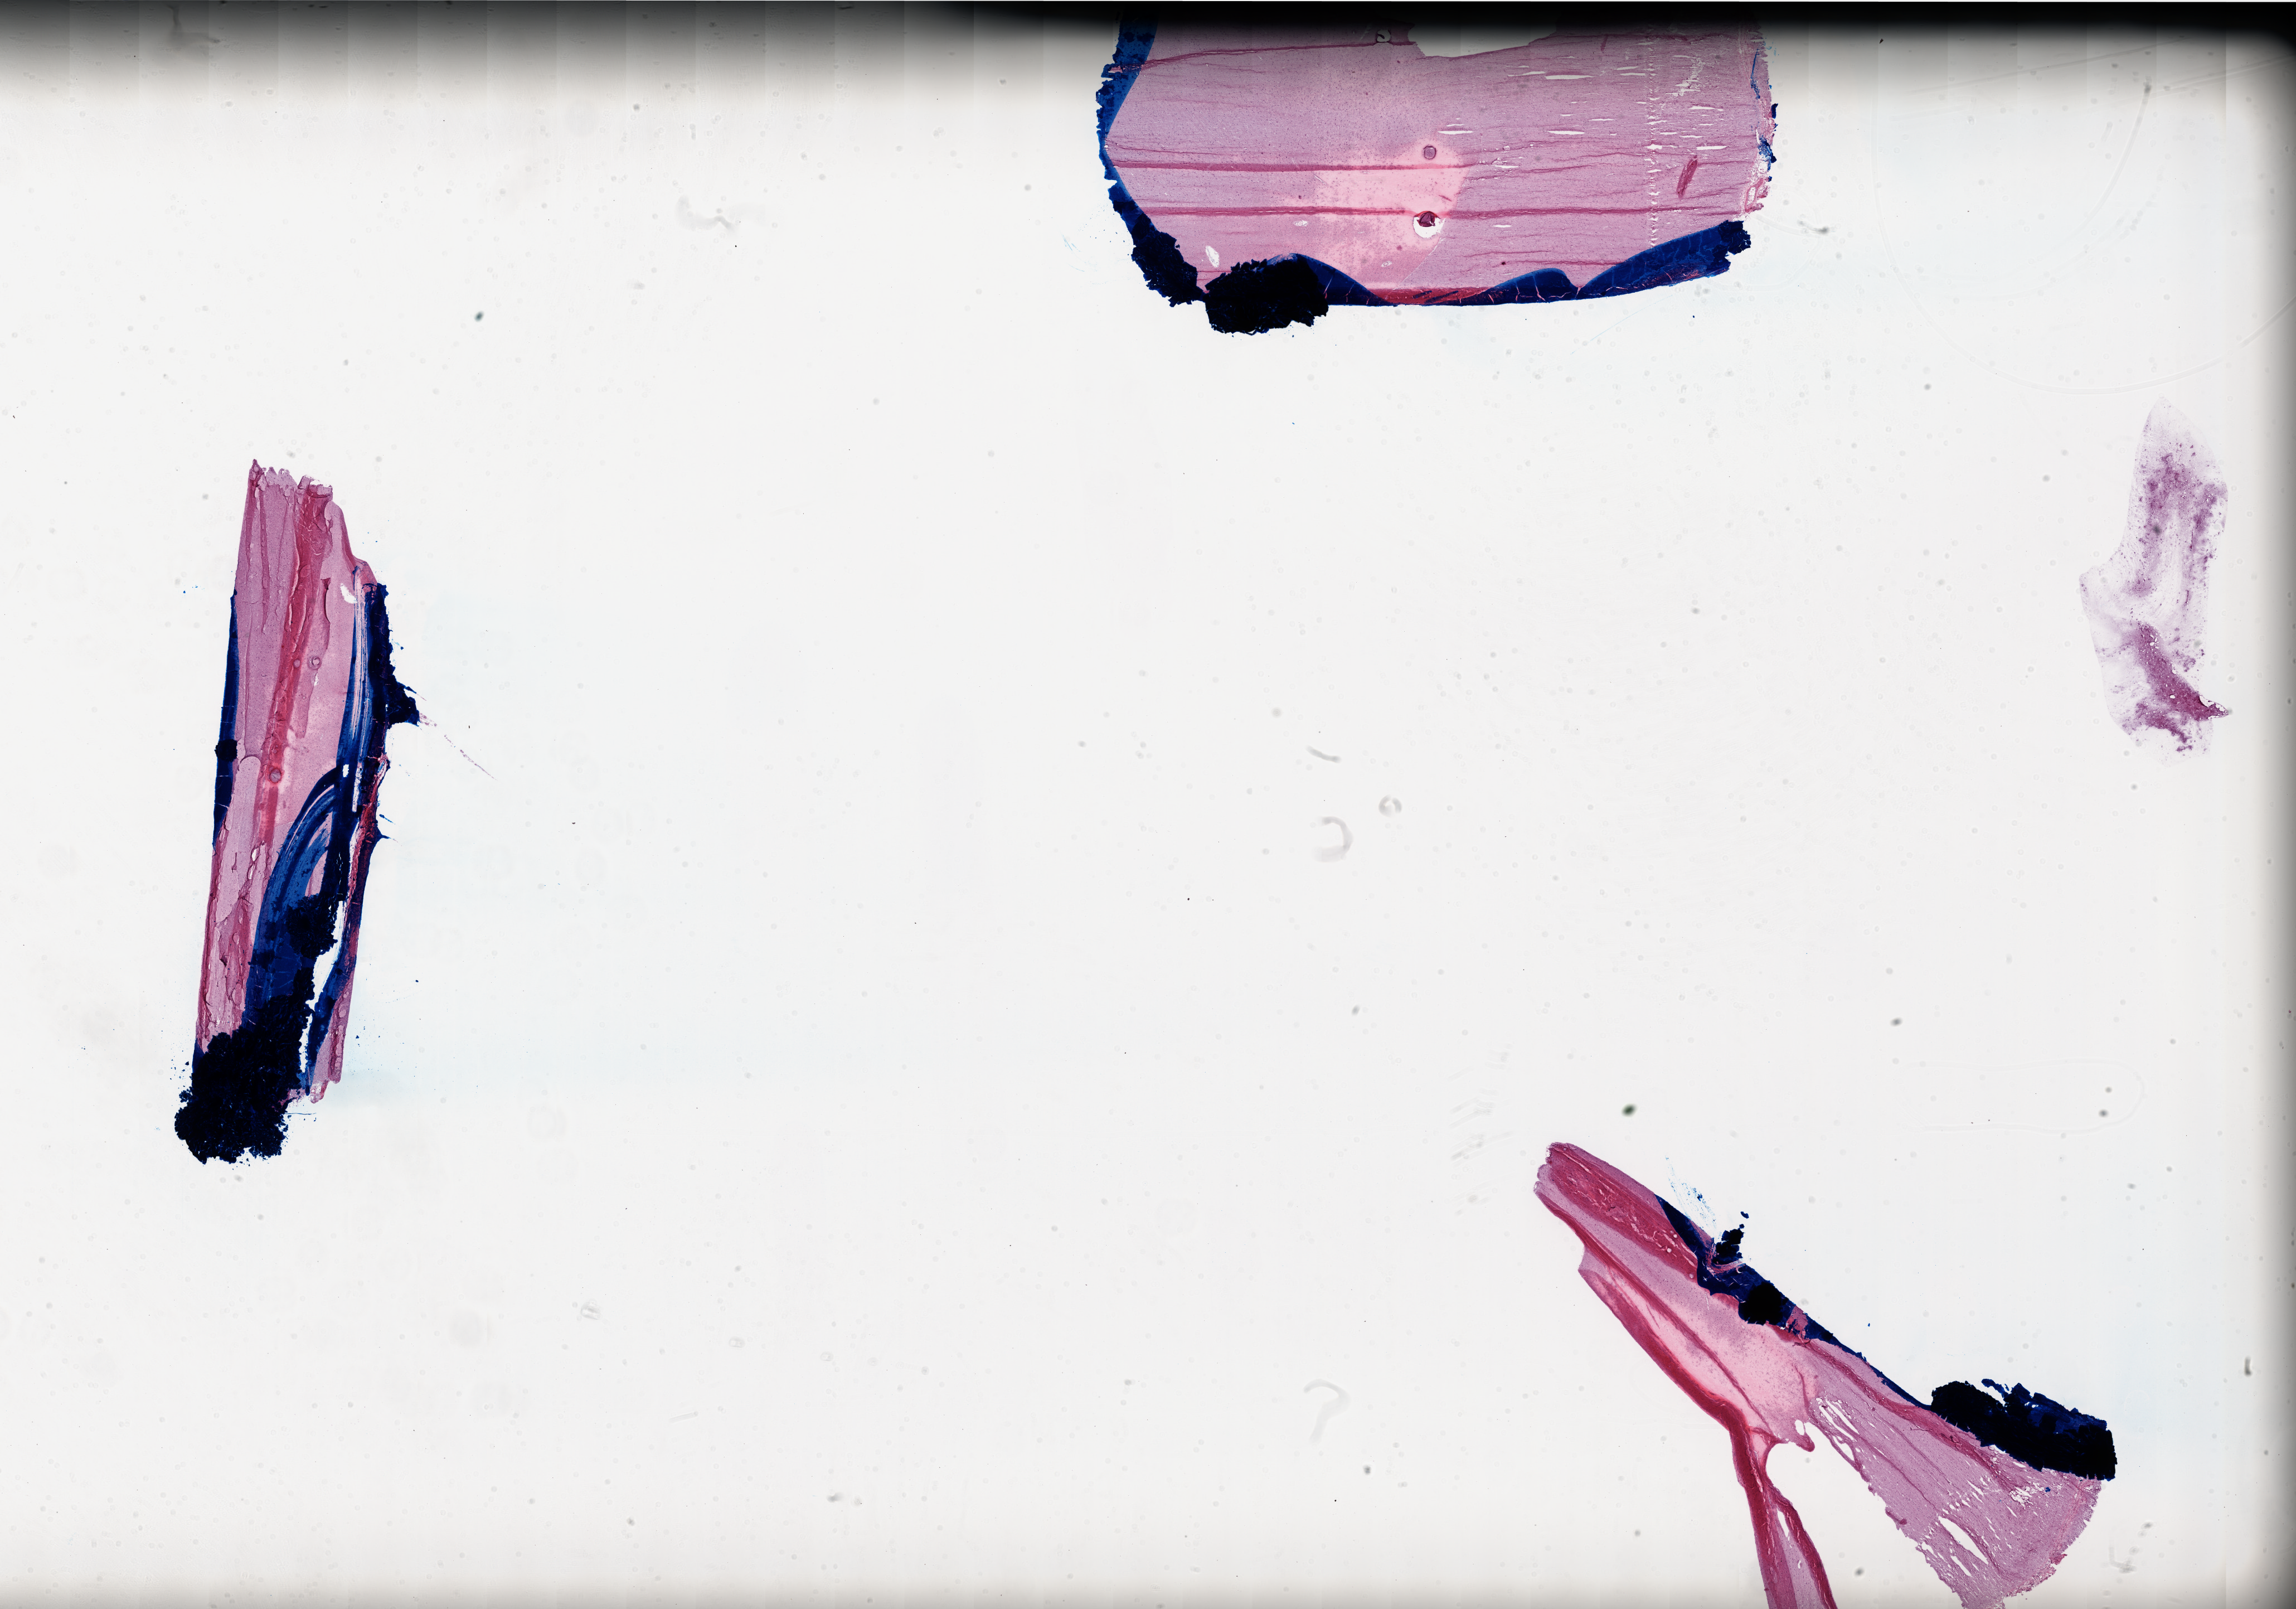
Digitized H&E tissue section (whole slide), low-resolution overview of the scanned area, about 33.0 x 23.1 mm. Frozen section from the top of the tissue portion. Primary tumour sample from the brain. Patient: male, age at initial diagnosis 44 years.
Diagnosis: Glioblastoma.